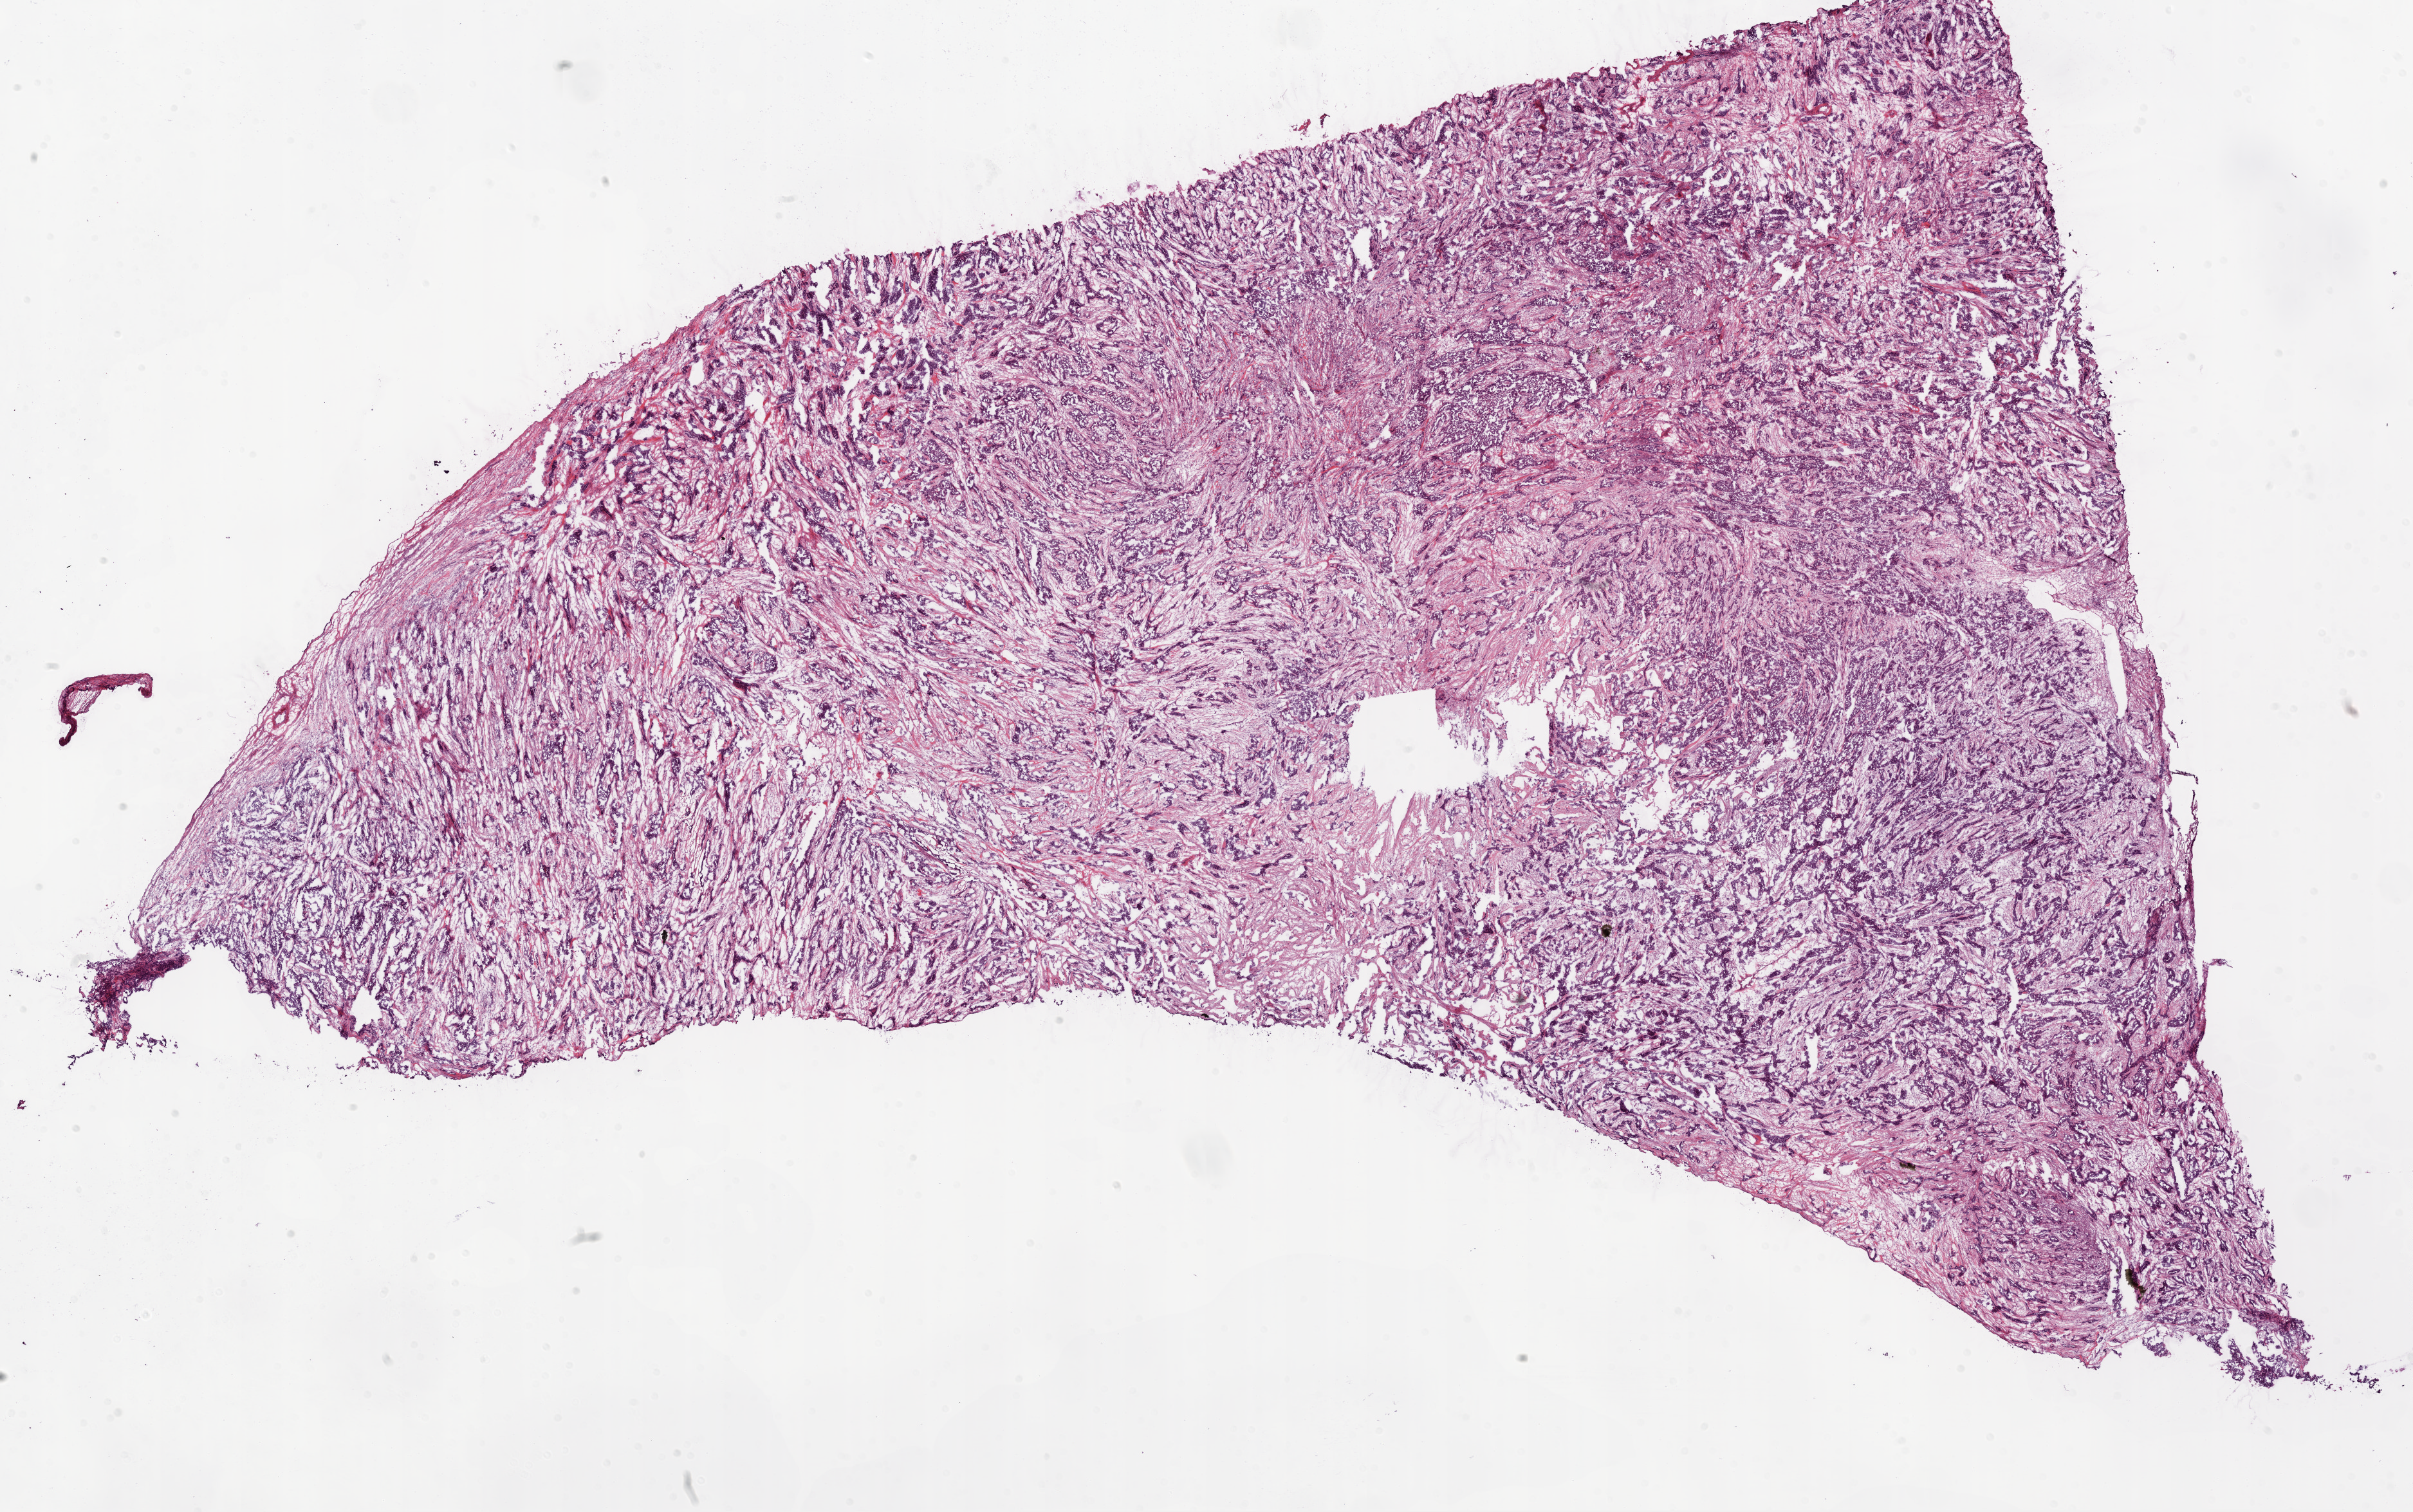
Digitized Hematoxylin and eosin (H&E) stained tissue section (whole slide) — shown as a low-resolution overview of the whole scanned area (about 30.1 x 18.9 mm, from a 20x scan), frozen section, ovary, primary tumour sample. Female patient; age at initial diagnosis 59 years. Histologic grade: G3 (poorly differentiated). Slide review estimates, as recorded: tumour cells 50%, tumour nuclei 90%, normal cells 0%, stromal cells 50%, necrosis 0%. Inflammatory infiltration, as recorded: lymphocyte infiltration 0%, monocyte infiltration 0%, neutrophil infiltration 0%.
FIGO stage: IIIC. Histologic diagnosis: Serous cystadenocarcinoma, NOS.